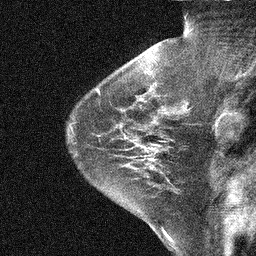
Breast MRI (dynamic contrast-enhanced), one sagittal slice; position 32 of 44 along the scan axis; dynamic contrast-enhanced study with each time point stored as its own series, time point 2 of 3 at this slice position (early post-contrast, ordered by acquisition time); 1.5 T; TE 5 ms, TR 10.3 ms; 256 × 256 image matrix, field of view 180 × 180 mm. Patient: female, 31 years. From the clinical record (not read from this slice): setting: breast cancer imaged before/during neoadjuvant chemotherapy; receptor status: HER2-positive.
Structures marked on this image (semi-automatically segmented with operator editing):
- analysis volume of interest (the breast-tissue region the enhancement analysis was run in; not a lesion): bounding box (x1, y1, x2, y2) in pixels: (136, 131, 181, 168)
- tumour enhancement mask (voxels above the 90 % enhancement threshold inside the analysis volume of interest): (142, 144, 160, 161)